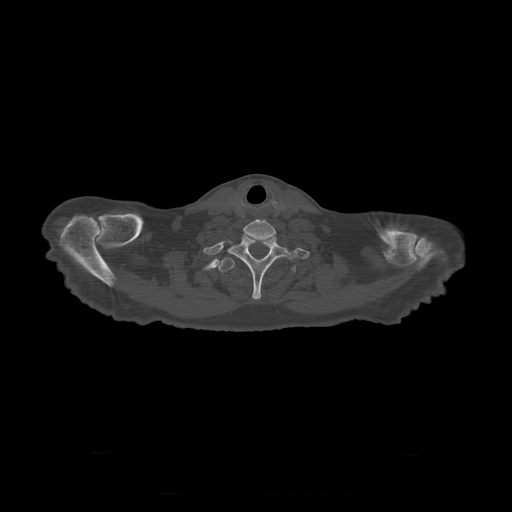
CT including the spine, one axial slice; slice 288 of 397 in the series (ordered by position); bone window (W 1800 / L 400 HU); 1.25 mm slice thickness; 512 × 512 image matrix. Patient age 73 years. Case-level facts recorded for this patient, not image findings: primary cancer: prostate.
Outlined on this slice (semi-automatic segmentation, software-assisted and operator-edited):
- T1 vertebra: box from (x=229, y=234) to (x=296, y=300) px
- T2 vertebra: (x=219, y=257)–(x=297, y=273)